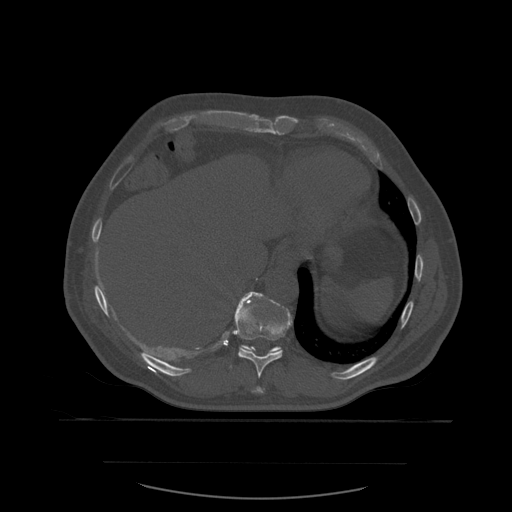
CT including the spine, one axial slice. Slice 314 of 590 in the series (ordered by position). Bone window (W 1800 / L 400 HU). 1.25 mm slice thickness. 512 × 512 image matrix, field of view 479 × 479 mm. Patient age 71 years. From the clinical record (not read from this slice): primary cancer: lung.
Structures marked on this image (semi-automatic segmentation, software-assisted and operator-edited):
- T10 vertebra: bounding box <230,292,293,379> (left, top, right, bottom; pixels)
- T11 vertebra: <239,294,293,353>
- T9 vertebra: <252,387,265,394>